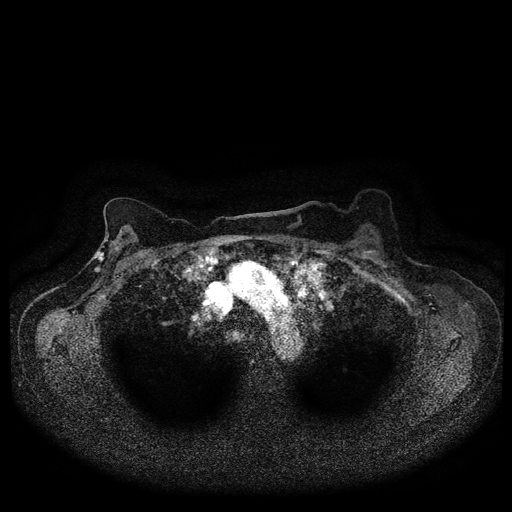
Breast MRI (dynamic contrast-enhanced, multi-phase), one axial slice. Slice 69 of 116 in the series (ordered by position). Dynamic contrast-enhanced series, time point 2 of 5 at this slice position (early post-contrast). 1.5 T. TE 2.7 ms, TR 5.4 ms. 2 mm slice thickness. 512 × 512 image matrix, field of view 340 × 340 mm. Female patient, age 72 years.
Outlined on this slice (semi-automatic segmentation, software-assisted and operator-edited):
- breast lesion (labelled 'tumour' in the annotation; benign lesions carry a separate 'benign' label): box from (x=92, y=249) to (x=106, y=274) px